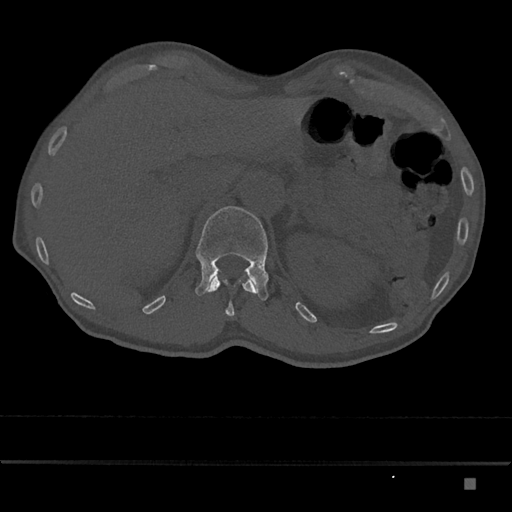
CT including the spine, one axial slice; position 572 of 797 along the scan axis; reconstruction kernel Br40s/3; 120 kVp; bone window (W 1800 / L 400 HU); 512 × 512 image matrix, field of view 390 × 390 mm. Male patient, age 72 years. Case-level facts recorded for this patient, not image findings: primary cancer: prostate.
Annotated regions visible in this slice (semi-automatic segmentation, software-assisted and operator-edited):
- L1 vertebra: bounding box (x1, y1, x2, y2) in pixels: (195, 206, 269, 301)
- T12 vertebra: (205, 276, 256, 317)